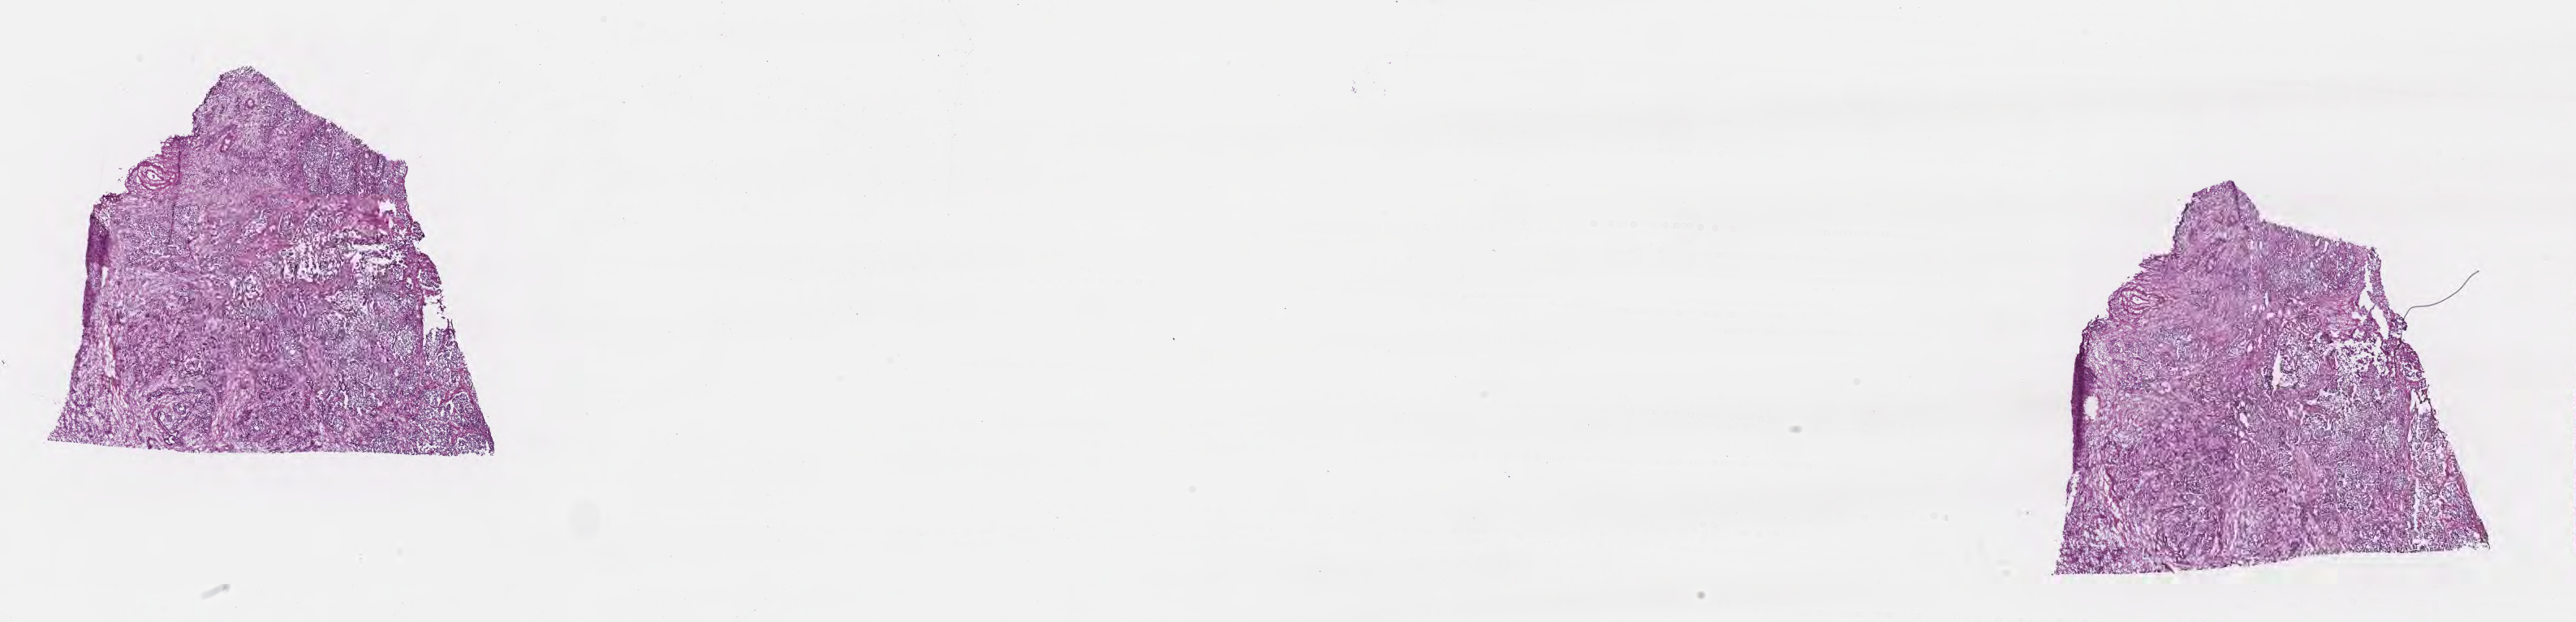
Hematoxylin and eosin (H&E) whole-slide image, shown as a low-resolution overview of the whole scanned area (about 25.7 x 6.2 mm), frozen section, specimen: primary tumor, anatomic site: head of pancreas. Patient: male, age at initial diagnosis 67 years. Tumor grade: G2 (moderately differentiated). Slide review estimates, as recorded: tumor cells 50%, tumor nuclei 60%, stromal cells 50%, necrosis 0%, normal cells 0%. Infiltration values recorded for this section: lymphocyte infiltration 0%, monocyte infiltration 0%, neutrophil infiltration 0%.
- diagnosis: Infiltrating duct carcinoma, NOS
- AJCC pathologic stage: Stage IIB
- section: bottom of the tissue portion